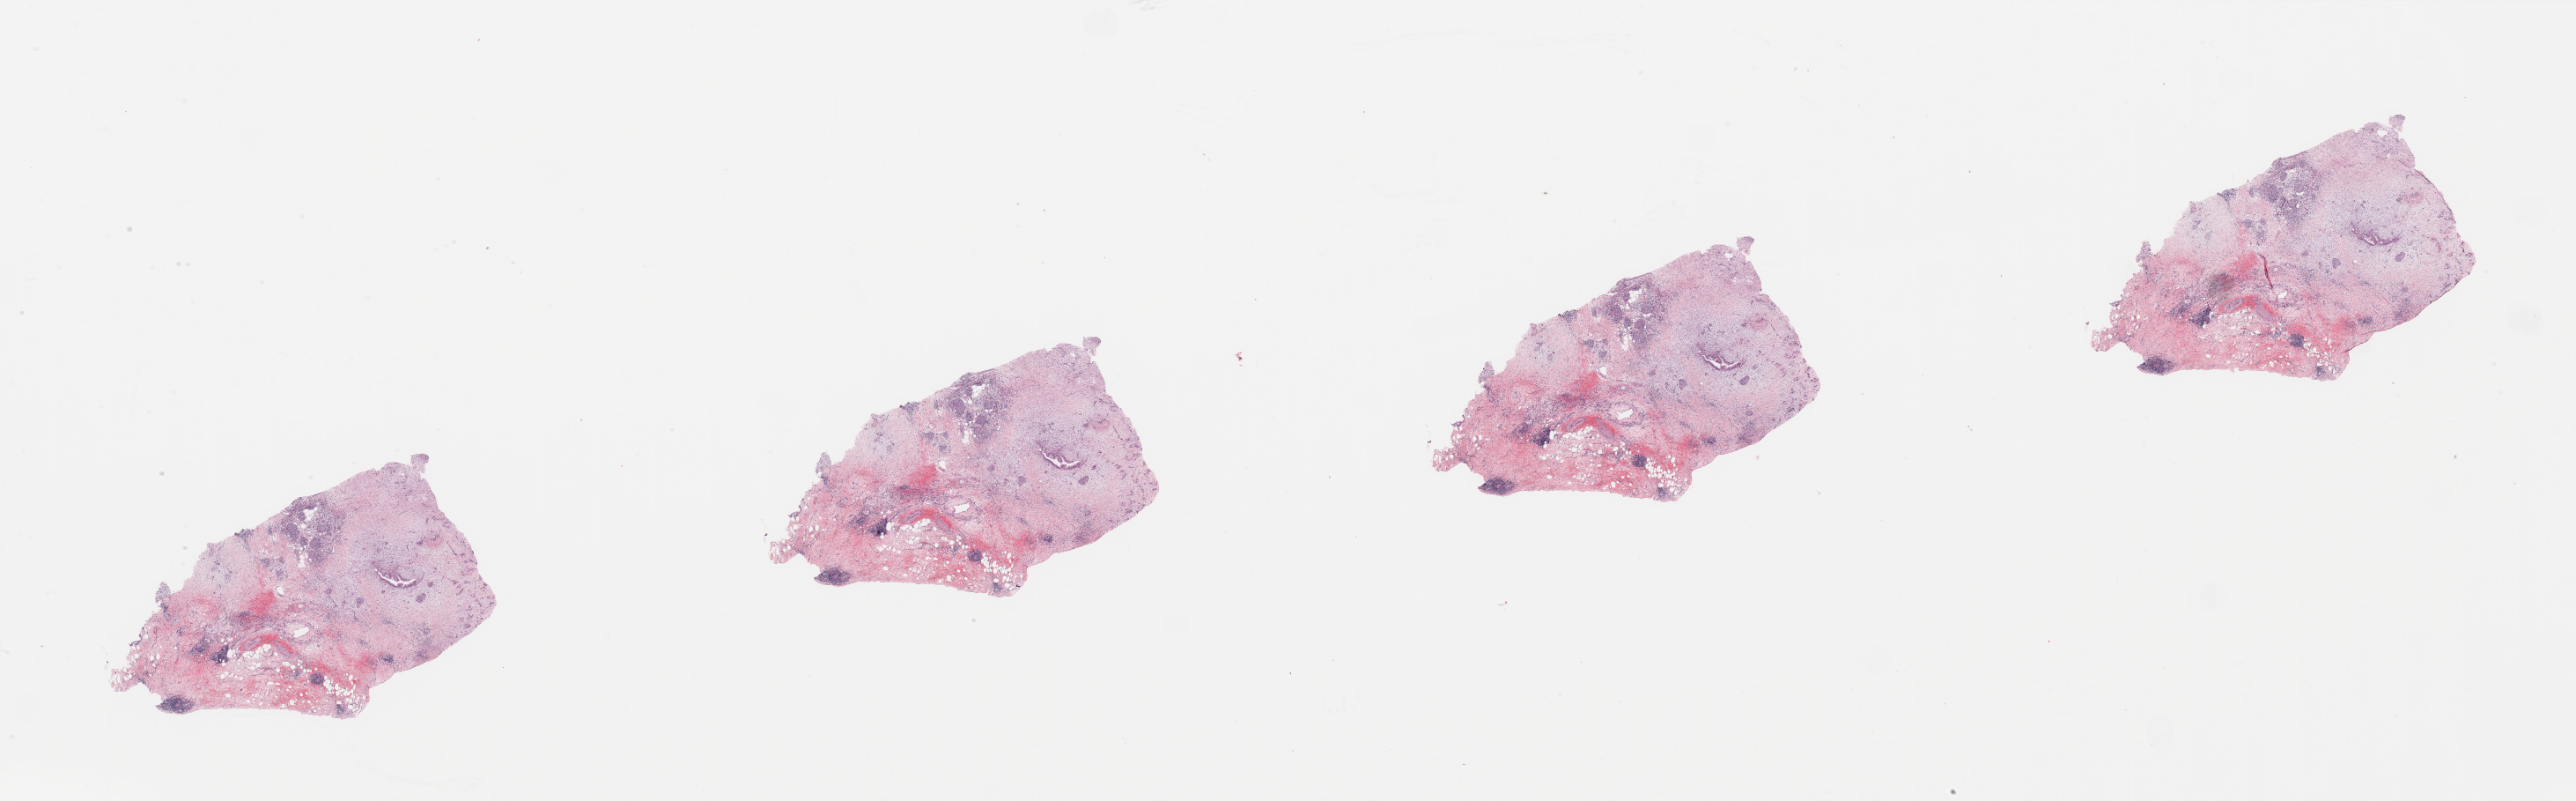
H&E whole-slide image — shown as a low-resolution overview of the whole scanned area (about 46.3 x 14.4 mm, from a 20x scan), tumour tissue sample, sampled site: pancreas. Patient: female, age 68 years. Histologic grade: G2 (moderately differentiated). Pathologist review of this section (percent, as recorded): tumour nuclei 20%, necrosis 0%.
Diagnosis: Infiltrating duct carcinoma, NOS. Primary tumour site (as recorded): head. AJCC pathologic stage: IIB.